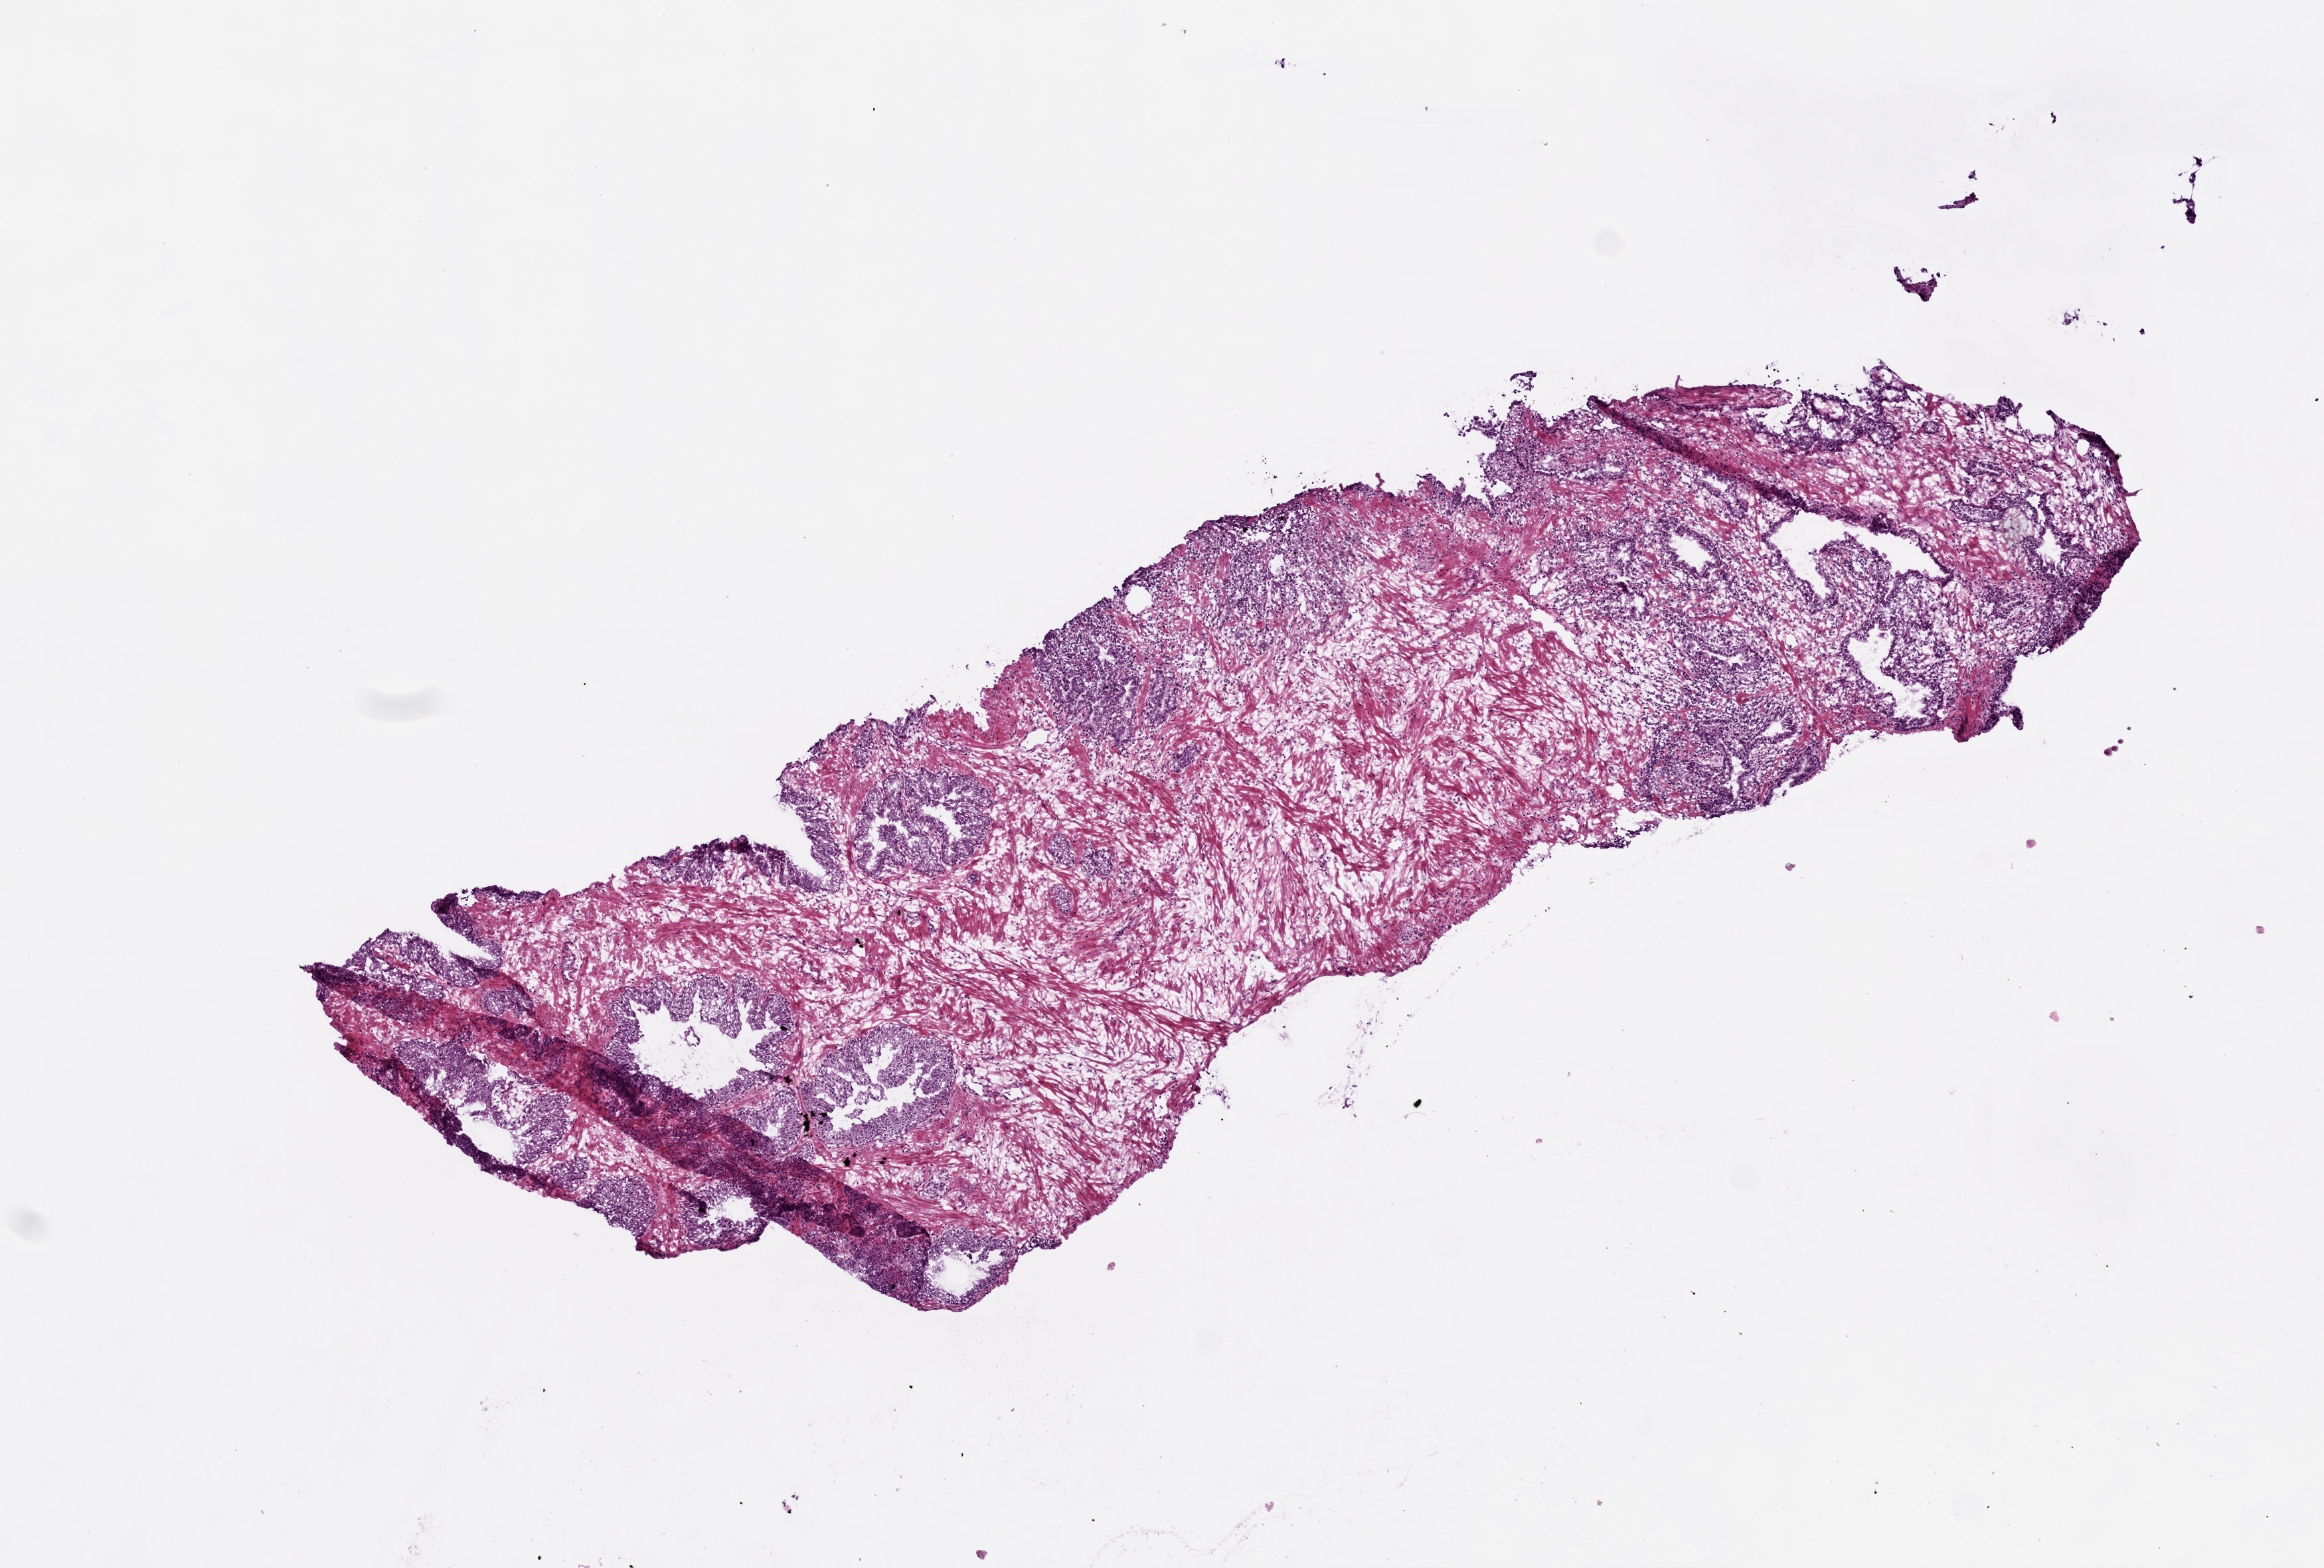
Digitized Hematoxylin and eosin (H&E) stained tissue section (whole slide) — shown as a low-resolution overview of the whole scanned area (about 7.0 x 4.7 mm, acquisition: 20x scan), frozen section, sample: solid tissue normal (non-tumour tissue), prostate. Male patient; age at initial diagnosis 55 years.
This section: solid tissue normal (non-tumour) sample from the same patient. Patient diagnosis: Acinar cell carcinoma (prostate gland).